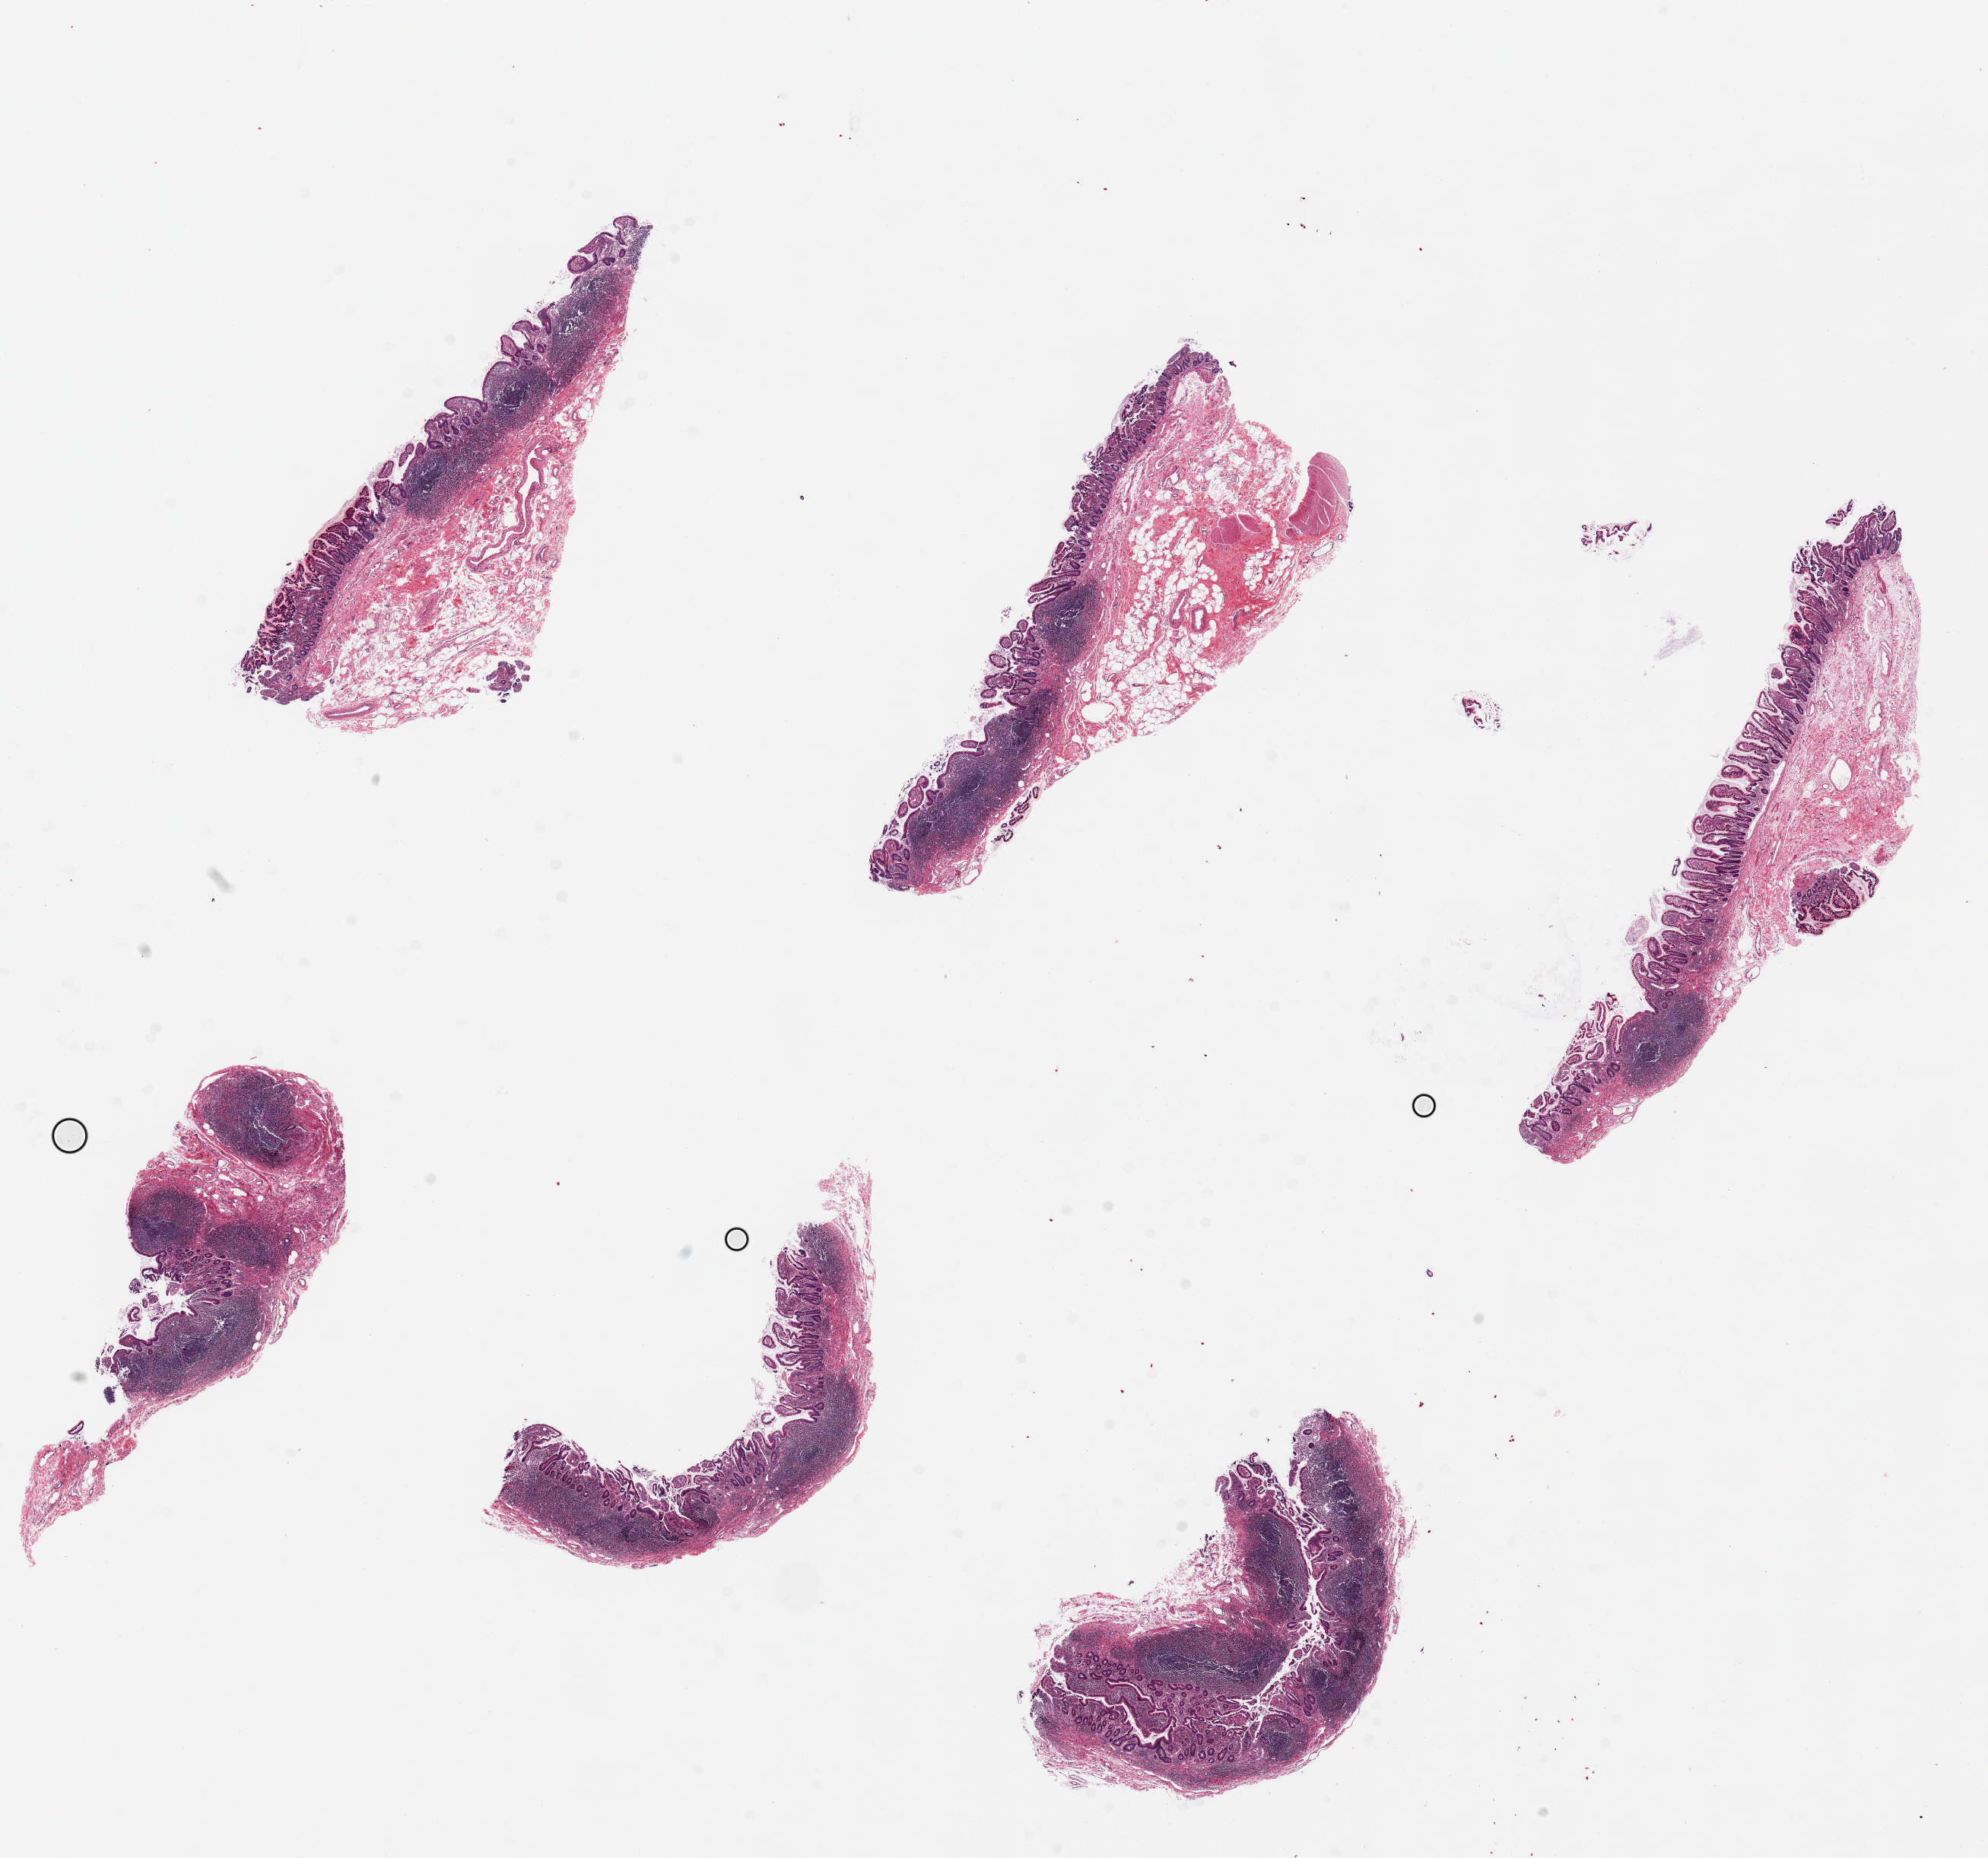
Whole-slide image, haematoxylin and eosin stain — a low-resolution overview of the entire scanned area, about 20.7 x 19.3 mm; PAXgene-fixed paraffin-embedded (PFPE) section; target tissue: ileum; tissue donor sample. Male donor.
- review note (as recorded): 6 pieces ~6x2mm; Extremely well preserved; mainly mucosa with lymphoid aggregates ~30-40% total specimen